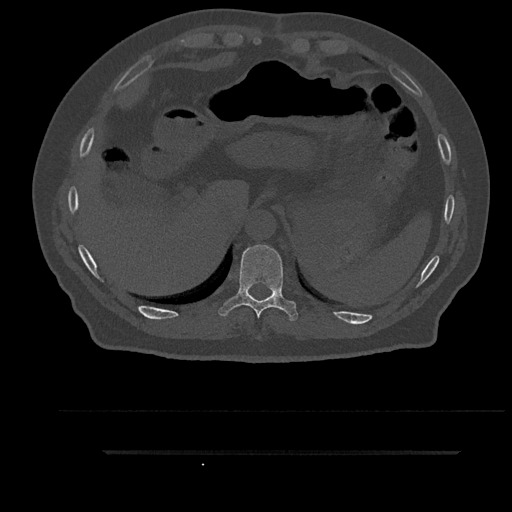
CT including the spine, one axial slice. Slice 367 of 797 in the series (ordered by position). 120 kVp. Bone window (W 1800 / L 400 HU). 0.5 mm slice thickness. 512 × 512 image matrix, field of view 432 × 432 mm. Male patient, age 63 years. From the clinical record (not read from this slice): primary cancer: renal.
Structures marked on this image (semi-automatically segmented with operator editing):
- T10 vertebra: bounding box <219,244,298,321> (left, top, right, bottom; pixels)